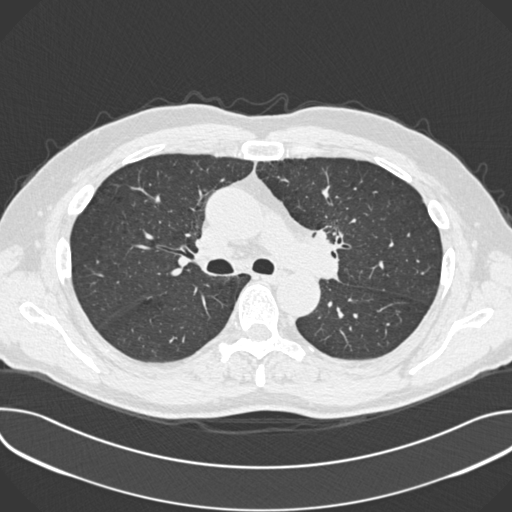
Low-dose screening chest CT, one axial slice. Slice 240 of 361 in the series (ordered by position). Reconstruction kernel B30f. Lung window (W 1500 / L -600 HU). 1 mm slice thickness. 512 × 512 image matrix, field of view 380 × 380 mm.
Outlined on this slice (expert manual segmentation):
- lesion 1 (tumor, upper lobe of left lung): bounding box [x1, y1, x2, y2] px = [315, 229, 345, 250]